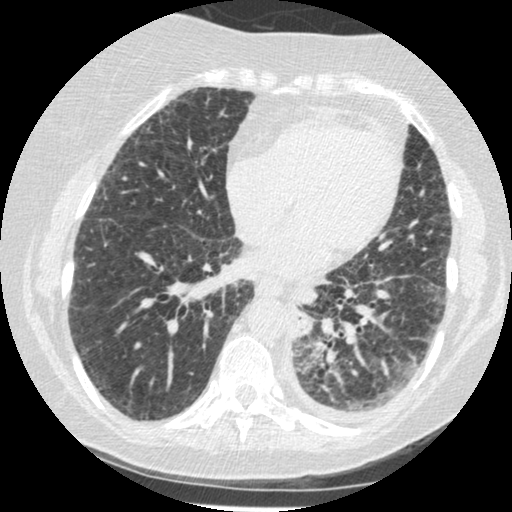
Low-dose screening chest CT, one axial slice. Slice 76 of 341 in the series (ordered by position). Reconstruction kernel STANDARD. 120 kVp. Lung window (W 1500 / L -600 HU). 512 × 512 image matrix, field of view 310 × 310 mm.
Outlined on this slice (outlined manually by an expert reader):
- lesion 1 (tumor, lower lobe of left lung): bounding box <294,323,311,336> (left, top, right, bottom; pixels)